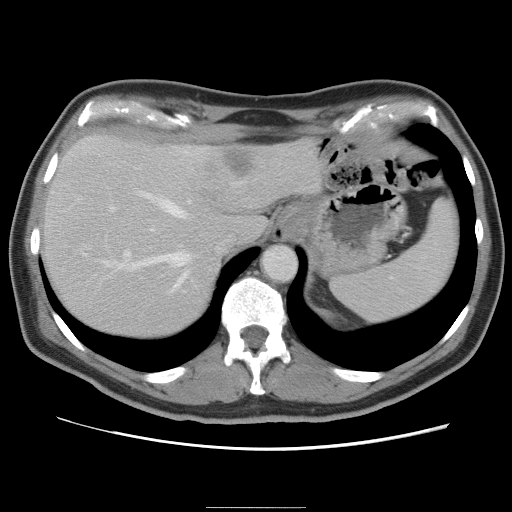
Contrast-enhanced abdominal CT, one axial slice. Position 64 of 87 along the scan axis. 120 kVp. Intravenous contrast given. Soft-tissue window (W 400 / L 40 HU). 512 × 512 image matrix, field of view 363 × 363 mm. Male patient, age 63 years. From the clinical record (not read from this slice): diagnosis: colorectal cancer liver metastases, imaged before liver resection; multiple liver metastases: no; largest metastasis: 9 cm; chemotherapy before resection: no.
Structures marked on this image (expert manual segmentation):
- hepatic veins: bounding box [x1, y1, x2, y2] px = [96, 182, 241, 294]
- liver: [40, 135, 324, 339]
- planned liver remnant (the part of the liver to remain after resection): [40, 160, 219, 339]
- portal vein (with intrahepatic branches): [102, 205, 185, 292]
- liver metastasis: [202, 148, 252, 178]